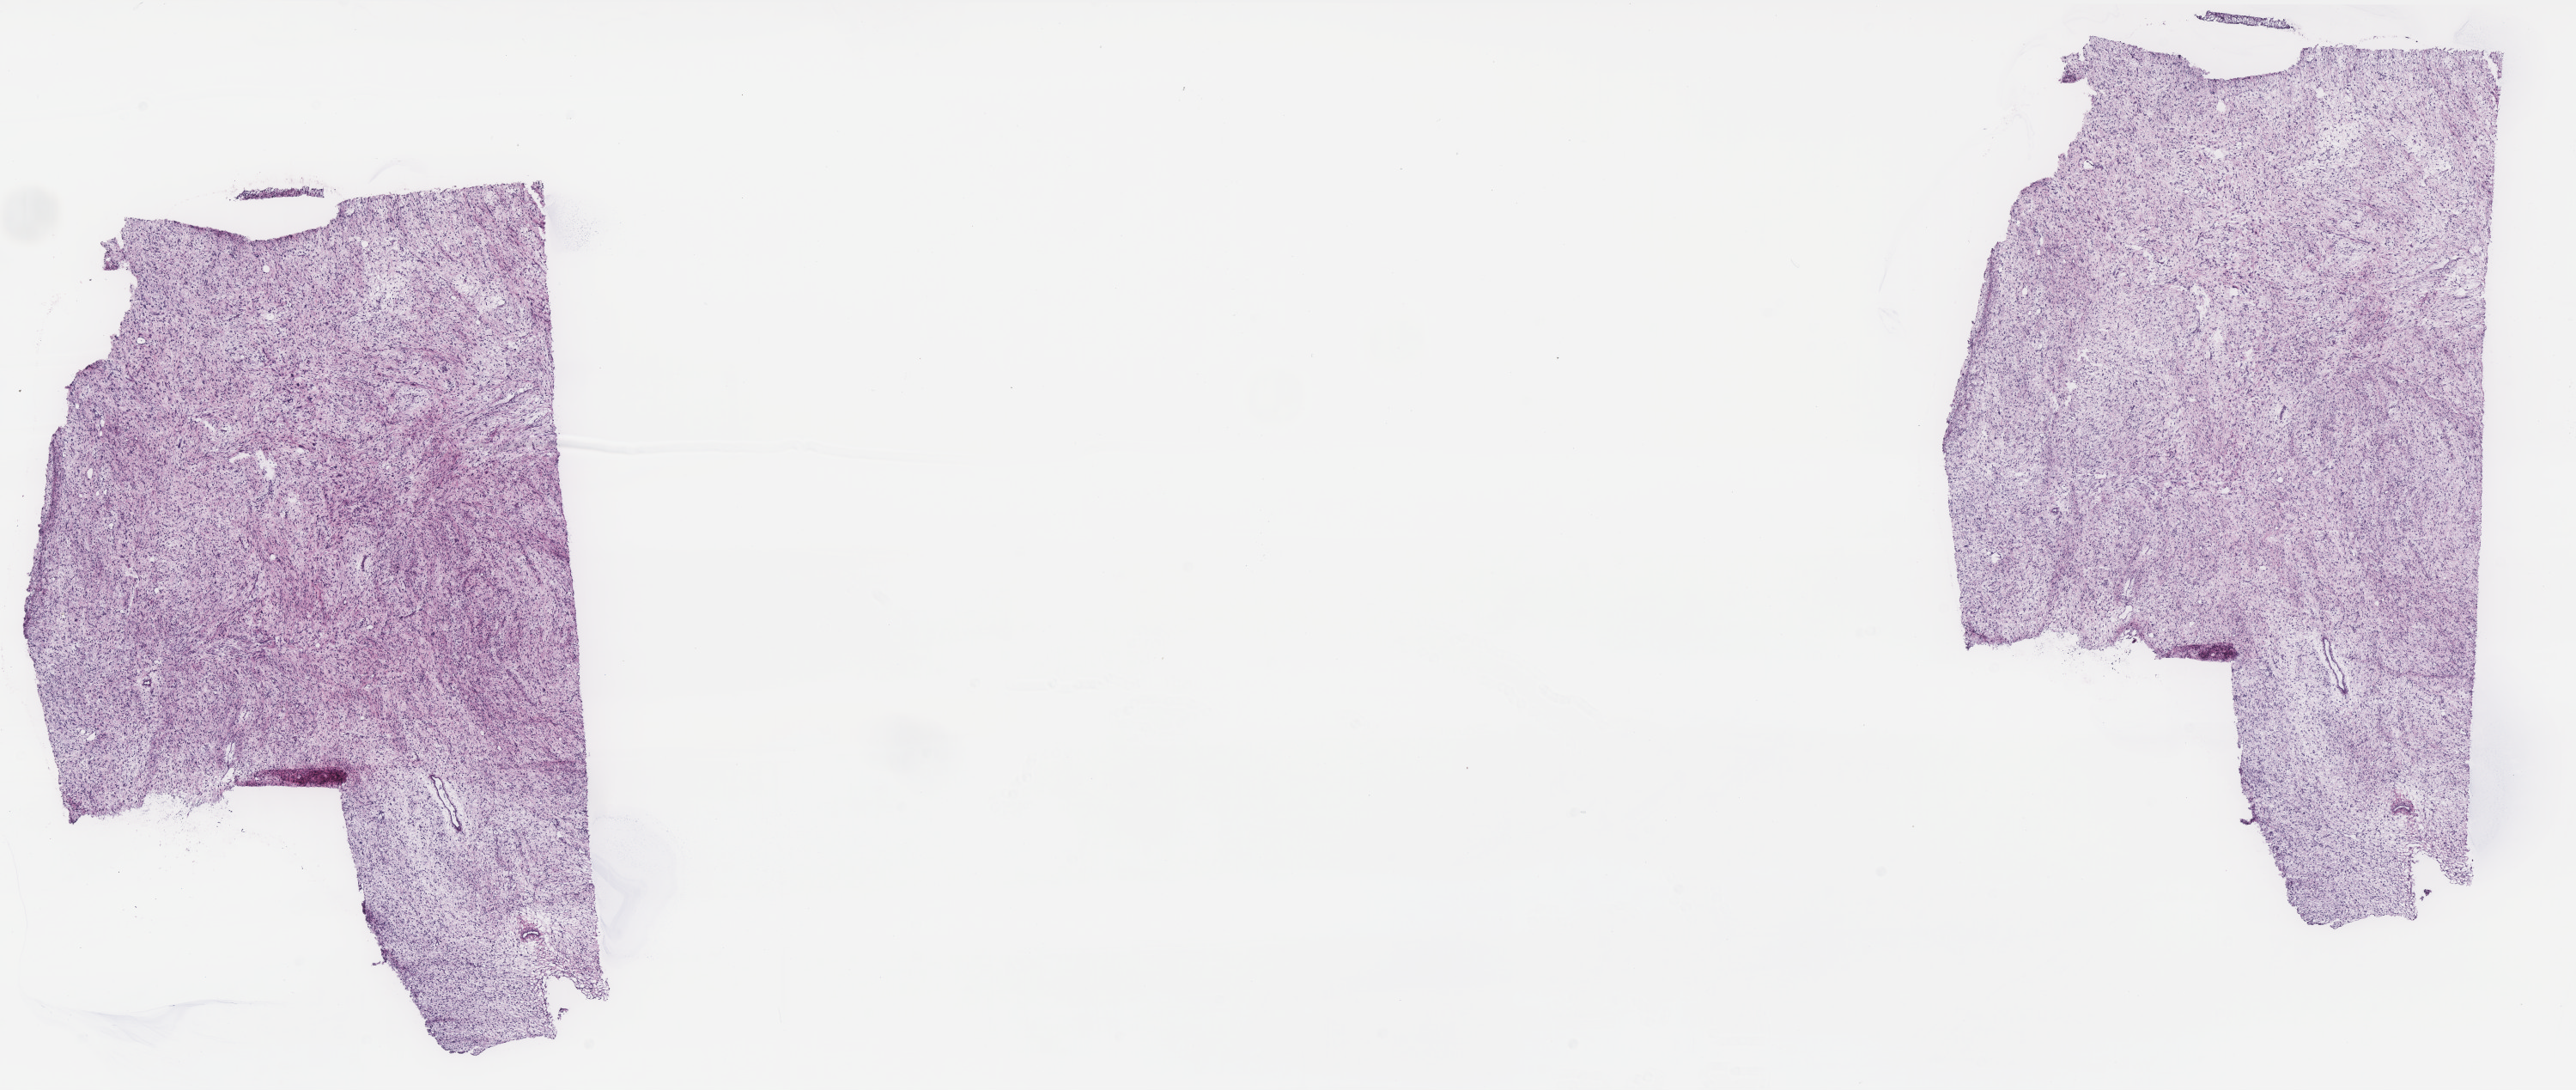
H&E whole-slide image, whole scanned area (about 24.1 x 10.2 mm, slide scanned at 40x) shown as a low-resolution overview. Frozen section from the top of the tissue portion. Sample: primary tumour, retroperitoneum and peritoneum. Male patient; age at initial diagnosis 67 years. Pathologist review of this section (percent, as recorded): tumour cells 90%, tumour nuclei 90%.
Diagnosis: Dedifferentiated liposarcoma.